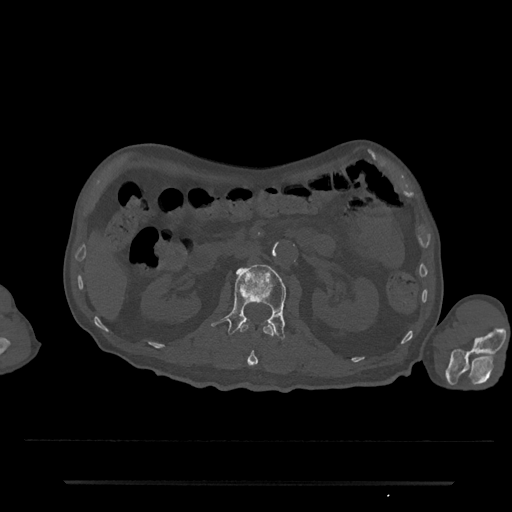
CT including the spine, one axial slice. Slice 83 of 797 in the series (ordered by position). Reconstruction kernel Br40s/3. 120 kVp. Bone window (W 1800 / L 400 HU). 0.5 mm slice thickness. 512 × 512 image matrix. Male patient, age 74 years. From the clinical record (not read from this slice): primary cancer: prostate.
Outlined on this slice (semi-automatic segmentation, software-assisted and operator-edited):
- L1 vertebra: bounding box (x1, y1, x2, y2) in pixels: (239, 322, 275, 367)
- L2 vertebra: (211, 264, 286, 340)